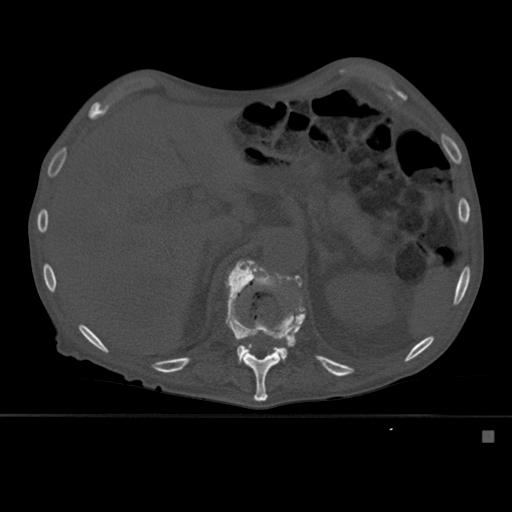
CT including the spine, one axial slice. Slice 271 of 527 in the series (ordered by position). Bone window (W 1800 / L 400 HU). 1.5 mm slice thickness. 512 × 512 image matrix. Patient: male, 78 years. Case-level facts recorded for this patient, not image findings: primary cancer: prostate.
Outlined on this slice (semi-automatic segmentation, software-assisted and operator-edited):
- L1 vertebra: box from (x=237, y=262) to (x=289, y=363) px
- T12 vertebra: (x=225, y=260)–(x=305, y=401)